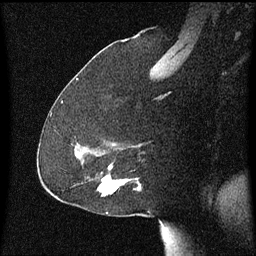
Breast MRI (dynamic contrast-enhanced), one sagittal slice; slice 36 of 60 in the series (ordered by position); dynamic contrast-enhanced series, image 2 of 3 at this slice position (ordered by acquisition); 1.5 T; TE 4.2 ms, TR 8.4 ms; 256 × 256 image matrix, field of view 200 × 200 mm. Patient: female, 59 years.
Structures marked on this image (semi-automatic segmentation, software-assisted and operator-edited):
- analysis volume of interest (the breast-tissue region the enhancement analysis was run in; not a lesion): box from (x=90, y=166) to (x=141, y=197) px
- tumour enhancement mask (voxels above the 70 % enhancement threshold inside the analysis volume of interest): (x=100, y=178)–(x=141, y=193)